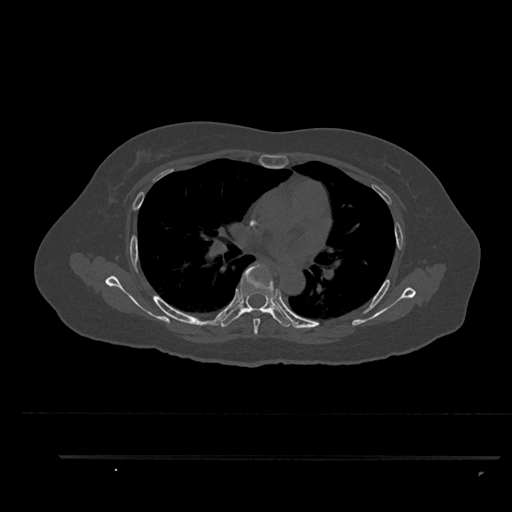
CT including the spine, one axial slice; position 574 of 797 along the scan axis; reconstruction kernel Br40s/3; bone window (W 1800 / L 400 HU); 0.5 mm slice thickness; 512 × 512 image matrix, field of view 408 × 408 mm. Female patient, age 44 years. Case-level facts recorded for this patient, not image findings: primary cancer: renal; vertebrae with lytic lesions (as recorded): L1.
Outlined on this slice (semi-automatically segmented with operator editing):
- T5 vertebra: bounding box [x1, y1, x2, y2] px = [253, 310, 260, 335]
- T6 vertebra: [220, 262, 295, 328]